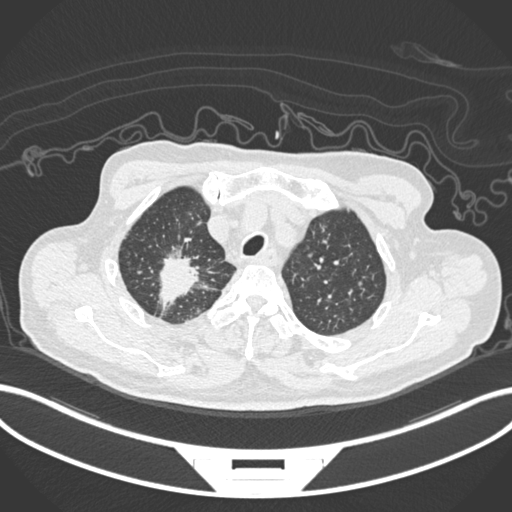
Chest CT, one axial slice. Slice 180 of 207 in the series (ordered by position). Reconstruction kernel B30f. Lung window (W 1500 / L -600 HU). 512 × 512 image matrix, field of view 400 × 400 mm. Patient: male, 69 years. From the clinical record (not read from this slice): clinical TNM (as recorded): T1c N1 M1.
Annotated regions visible in this slice (bounding box drawn by a radiologist):
- lung tumour (recorded histology: adenocarcinoma): bounding box (x1, y1, x2, y2) in pixels: (149, 250, 208, 304)